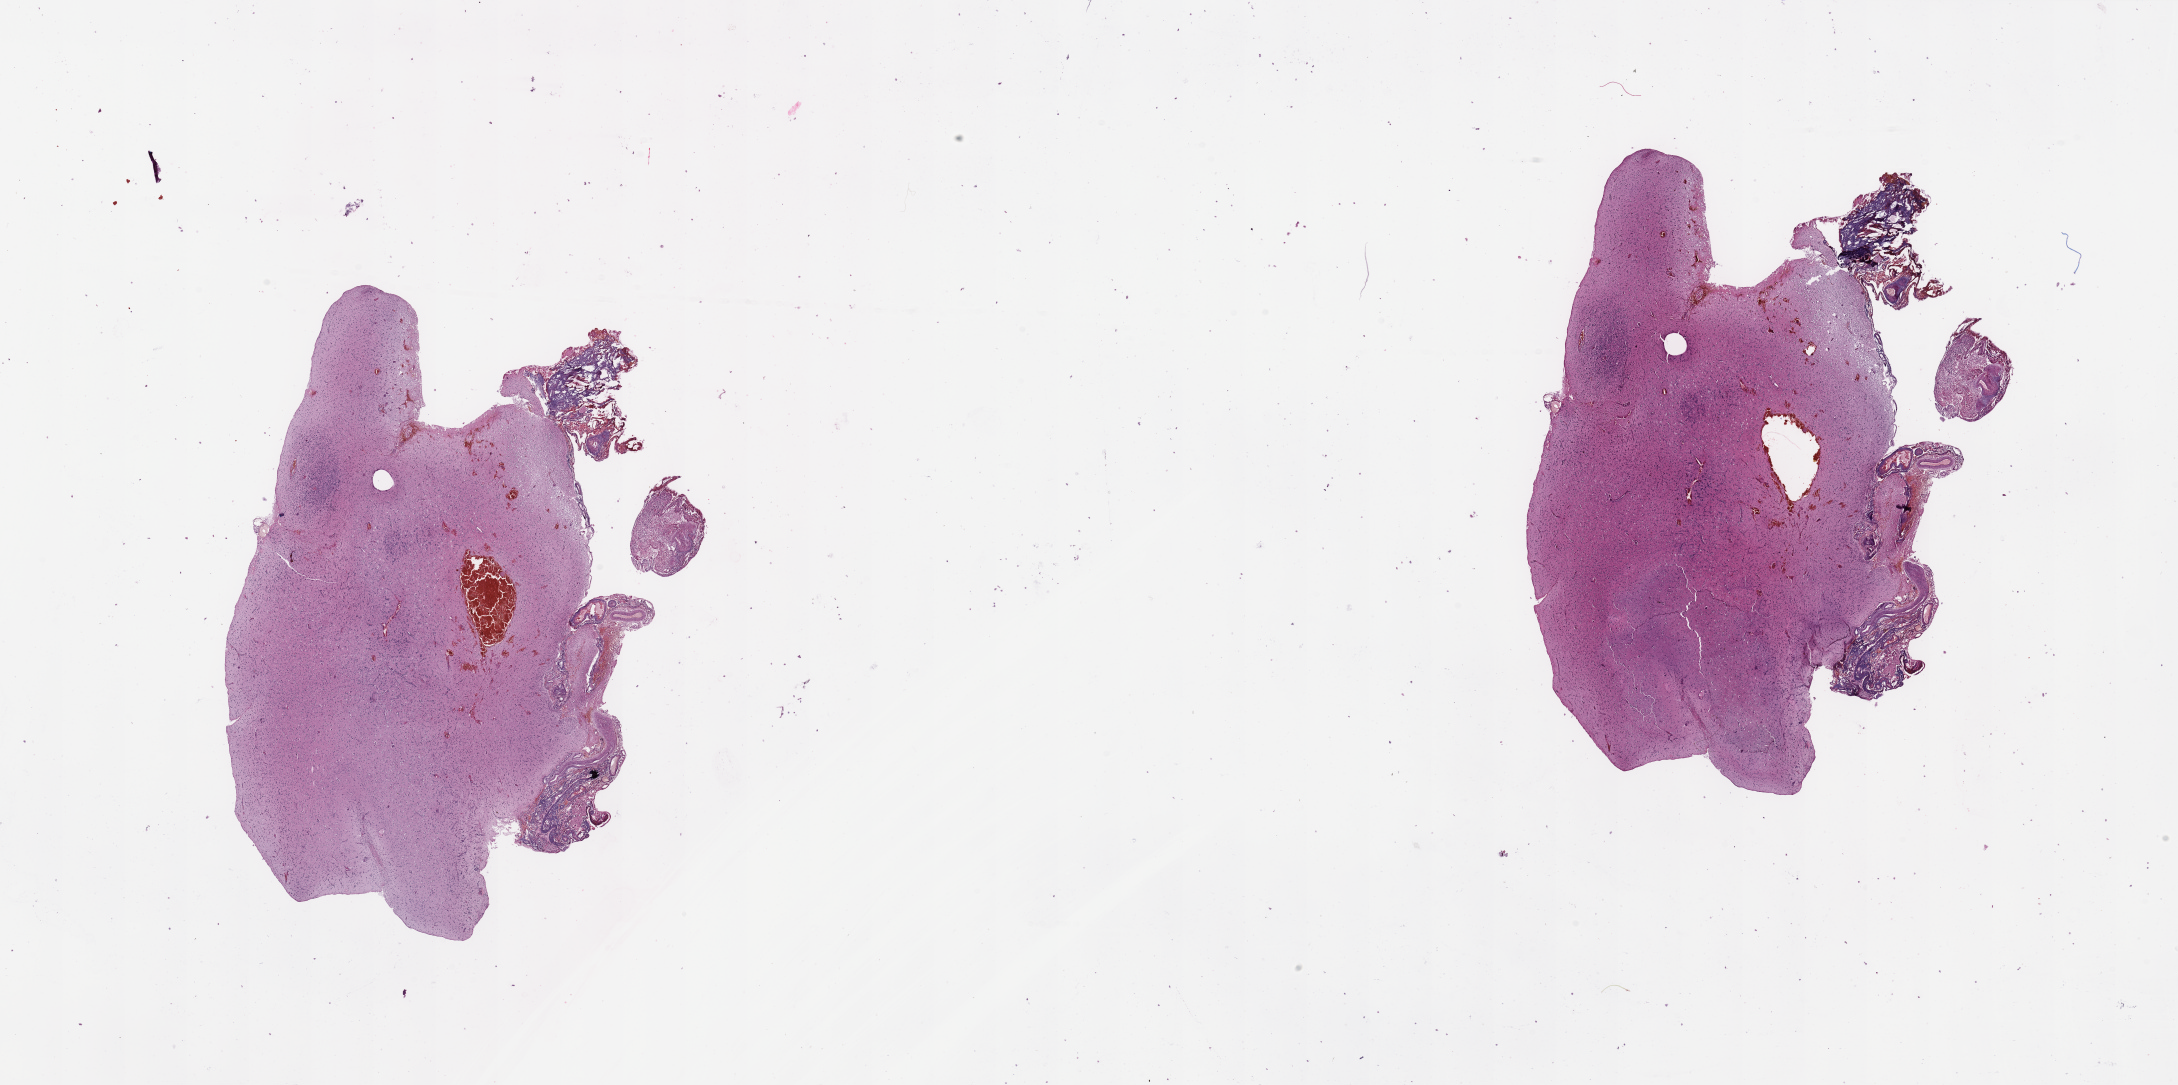
Hematoxylin and eosin (H&E) stained whole-slide image, whole scanned area (about 34.5 x 17.2 mm, acquisition: 20x scan) shown as a low-resolution overview. Tumour tissue sample, sampled site: frontal lobe. 77-year-old male patient. Slide review estimates, as recorded: tumour nuclei 40%, necrosis 5%.
Diagnosis: Glioblastoma.